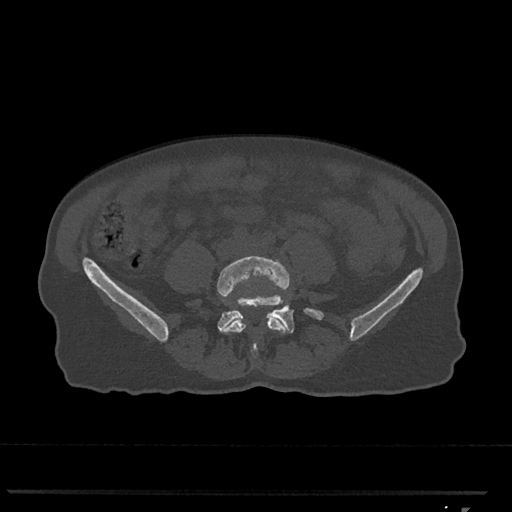
CT including the spine, one axial slice; position 179 of 793 along the scan axis; reconstruction kernel Br40s/3; 120 kVp; bone window (W 1800 / L 400 HU); 512 × 512 image matrix, field of view 380 × 380 mm. Patient: female, 62 years. From the clinical record (not read from this slice): primary cancer: renal.
Annotated regions visible in this slice (semi-automatic segmentation, software-assisted and operator-edited):
- L4 vertebra: box from (x=217, y=256) to (x=290, y=358) px
- L5 vertebra: (x=218, y=295)–(x=323, y=333)